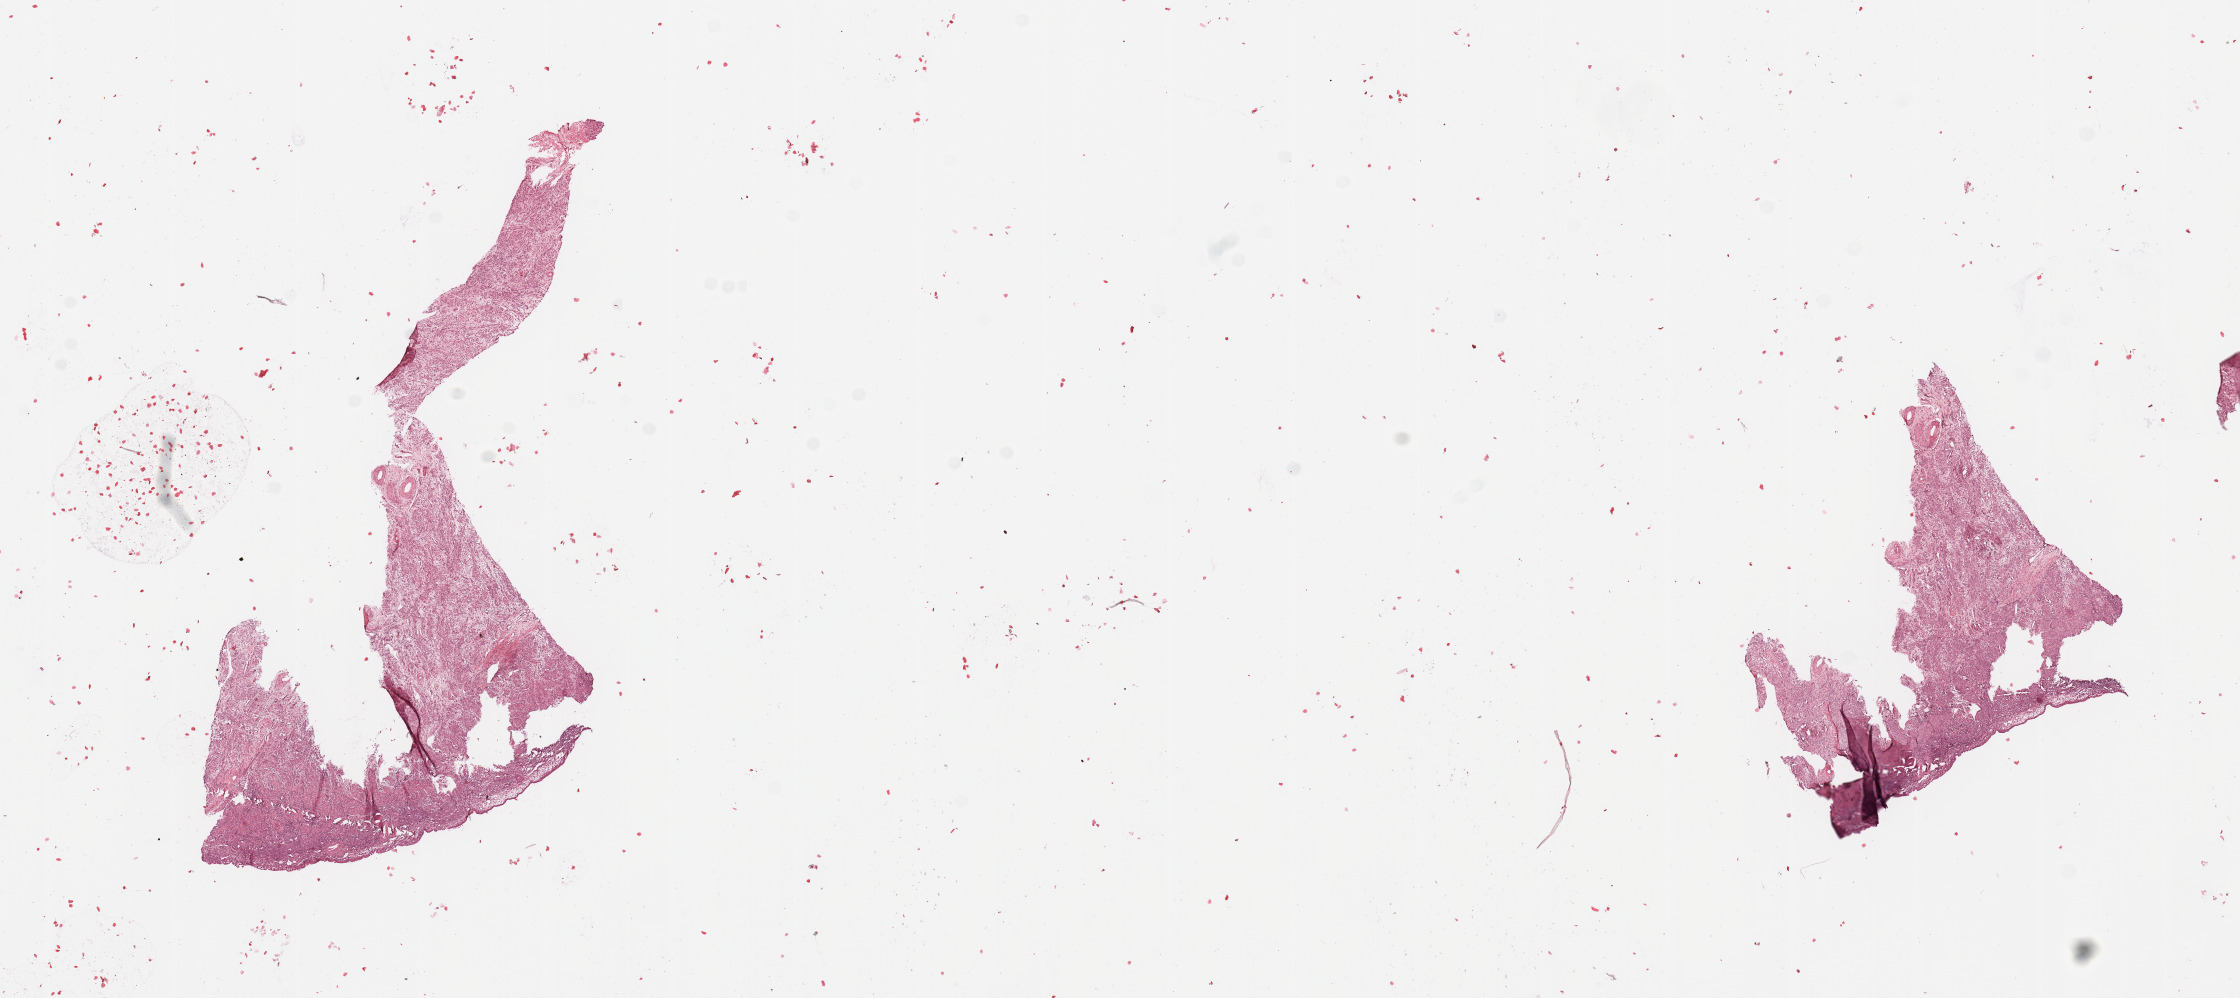
Whole-slide histology image, Hematoxylin and eosin (H&E) stained, shown as a low-resolution overview of the whole scanned area (about 17.7 x 7.9 mm, acquisition: 20x scan), normal (non-tumour) tissue sample, uterus. Female, 61 y/o.
This section: normal (non-tumour) tissue from the same patient. Patient diagnosis: Endometrioid adenocarcinoma, NOS.